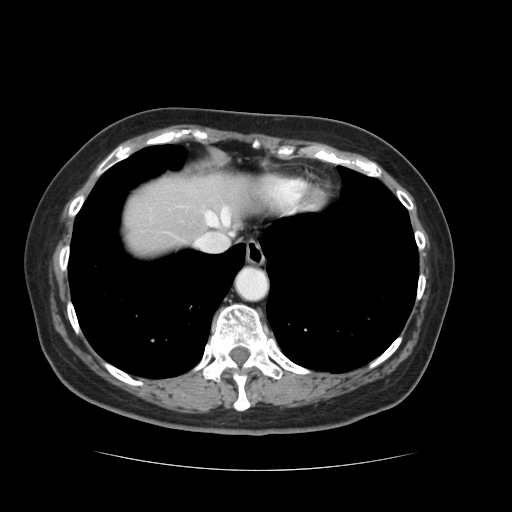
Contrast-enhanced abdominal CT, one axial slice. Slice 113 of 128 in the series (ordered by position). 120 kVp. Intravenous contrast given. Soft-tissue window (W 400 / L 40 HU). 2.5 mm slice thickness. 512 × 512 image matrix. Female patient, age 67 years. From the clinical record (not read from this slice): diagnosis: colorectal cancer liver metastases, imaged before liver resection; multiple liver metastases: yes; largest metastasis: 3 cm; disease in both lobes: yes.
Annotated regions visible in this slice (expert manual segmentation):
- hepatic veins: bounding box <195,207,233,251> (left, top, right, bottom; pixels)
- liver: <124,173,245,254>
- planned liver remnant (the part of the liver to remain after resection): <125,175,245,254>